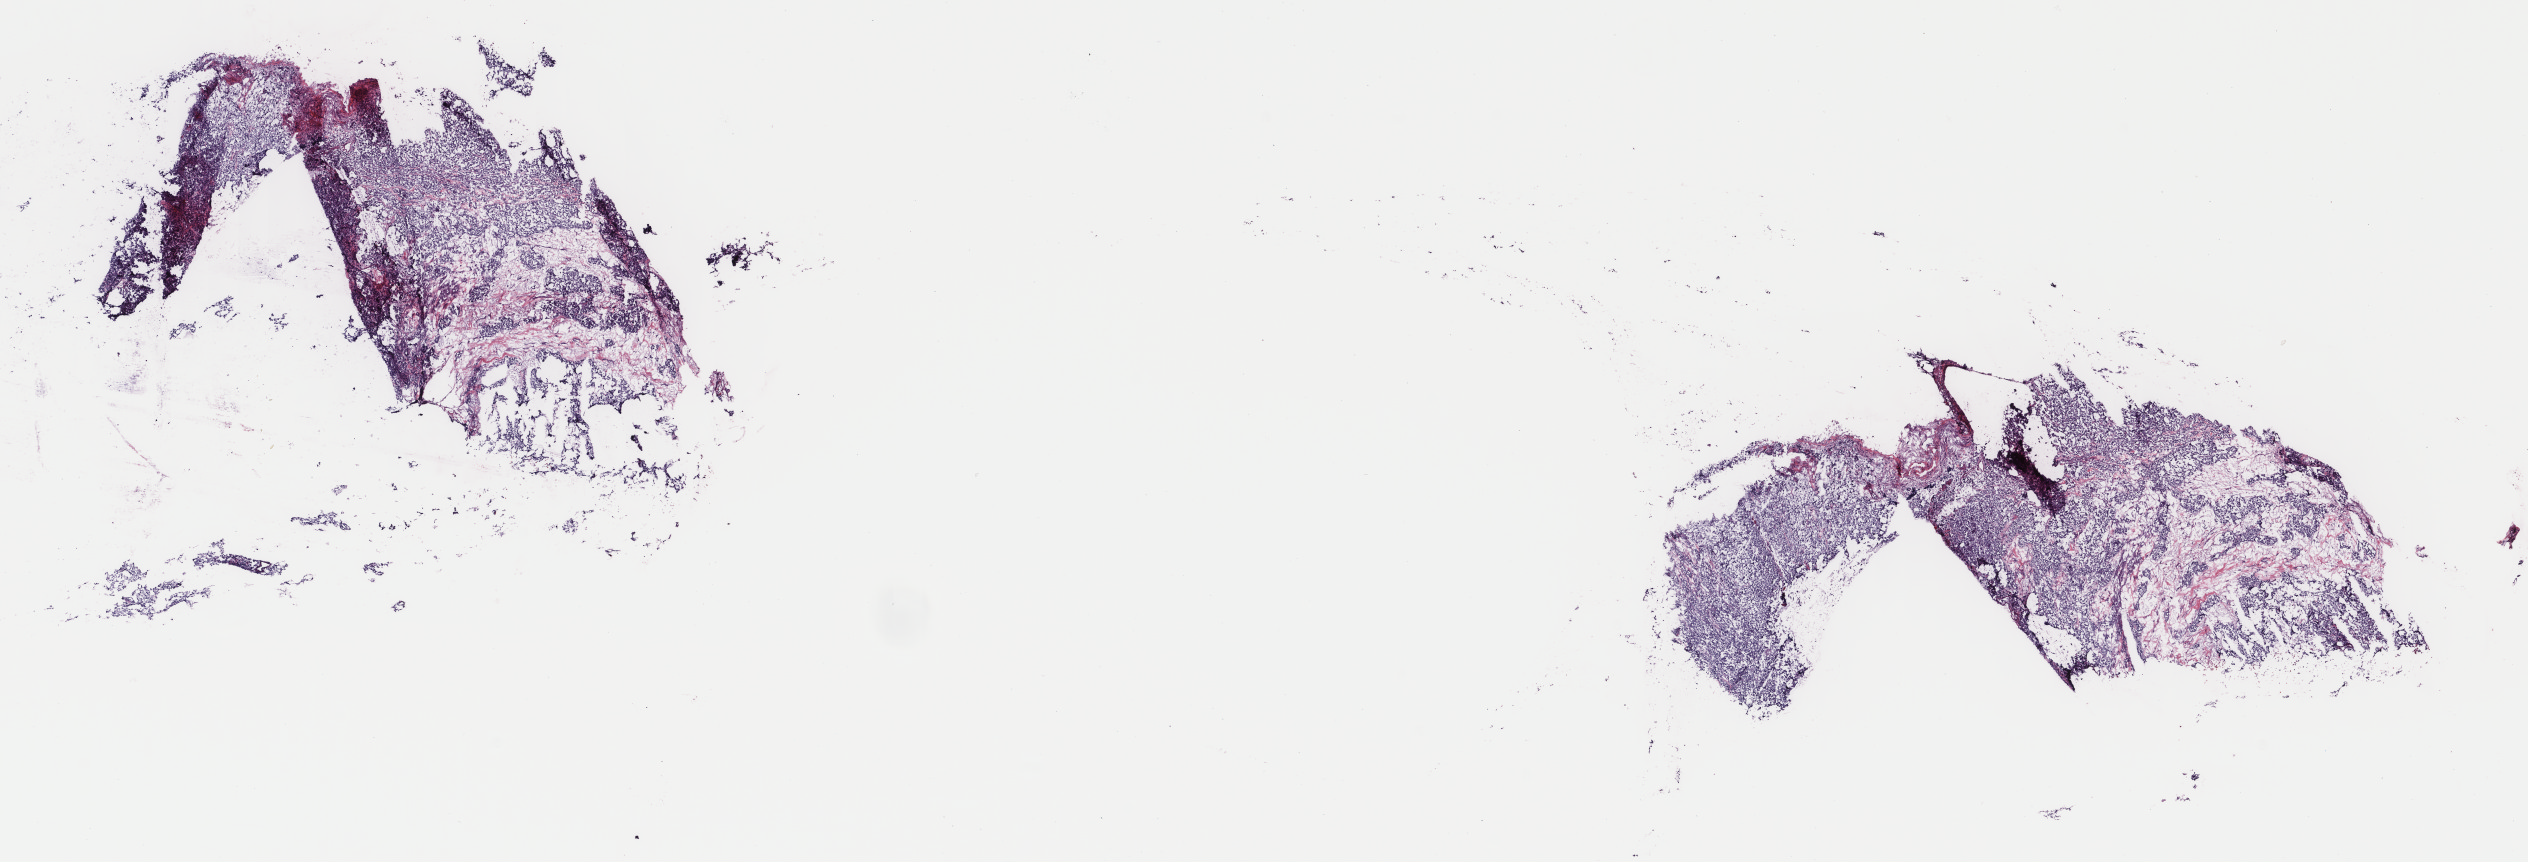
Digitized Hematoxylin and eosin (H&E) stained tissue section (whole slide), whole scanned area (about 20.1 x 6.8 mm, acquisition: 40x scan) shown as a low-resolution overview; frozen section; sample: primary tumour, other endocrine glands and related structures. Female patient; age at initial diagnosis 61 years. Pathologist review of this section (percent, as recorded): tumour cells 100%, tumour nuclei 80%, normal cells 0%, stromal cells 0%, necrosis 0%. Infiltration values recorded for this section: lymphocyte infiltration 1%, monocyte infiltration 0%, neutrophil infiltration 0%.
Diagnosis: Pheochromocytoma, malignant (aortic body and other paraganglia).